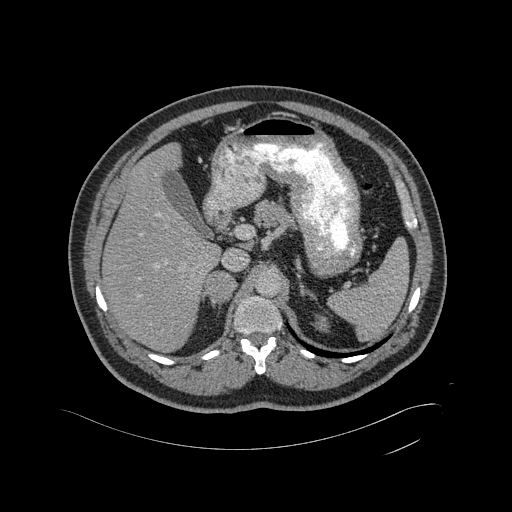
Contrast-enhanced abdominal CT, one axial slice. Position 320 of 433 along the scan axis. 120 kVp. Intravenous contrast given. Soft-tissue window (W 400 / L 40 HU). 2 mm slice thickness. 512 × 512 image matrix, field of view 500 × 500 mm. Male patient, age 56 years. Case-level facts recorded for this patient, not image findings: diagnosis: adrenocortical carcinoma; tumour side: right adrenal; tumour size at pathology: 11.6 cm; Ki-67 index: 50 %; stage (as recorded): 3.
Outlined on this slice (semi-automatic segmentation, software-assisted and operator-edited):
- mass: bounding box (x1, y1, x2, y2) in pixels: (207, 272, 236, 303)